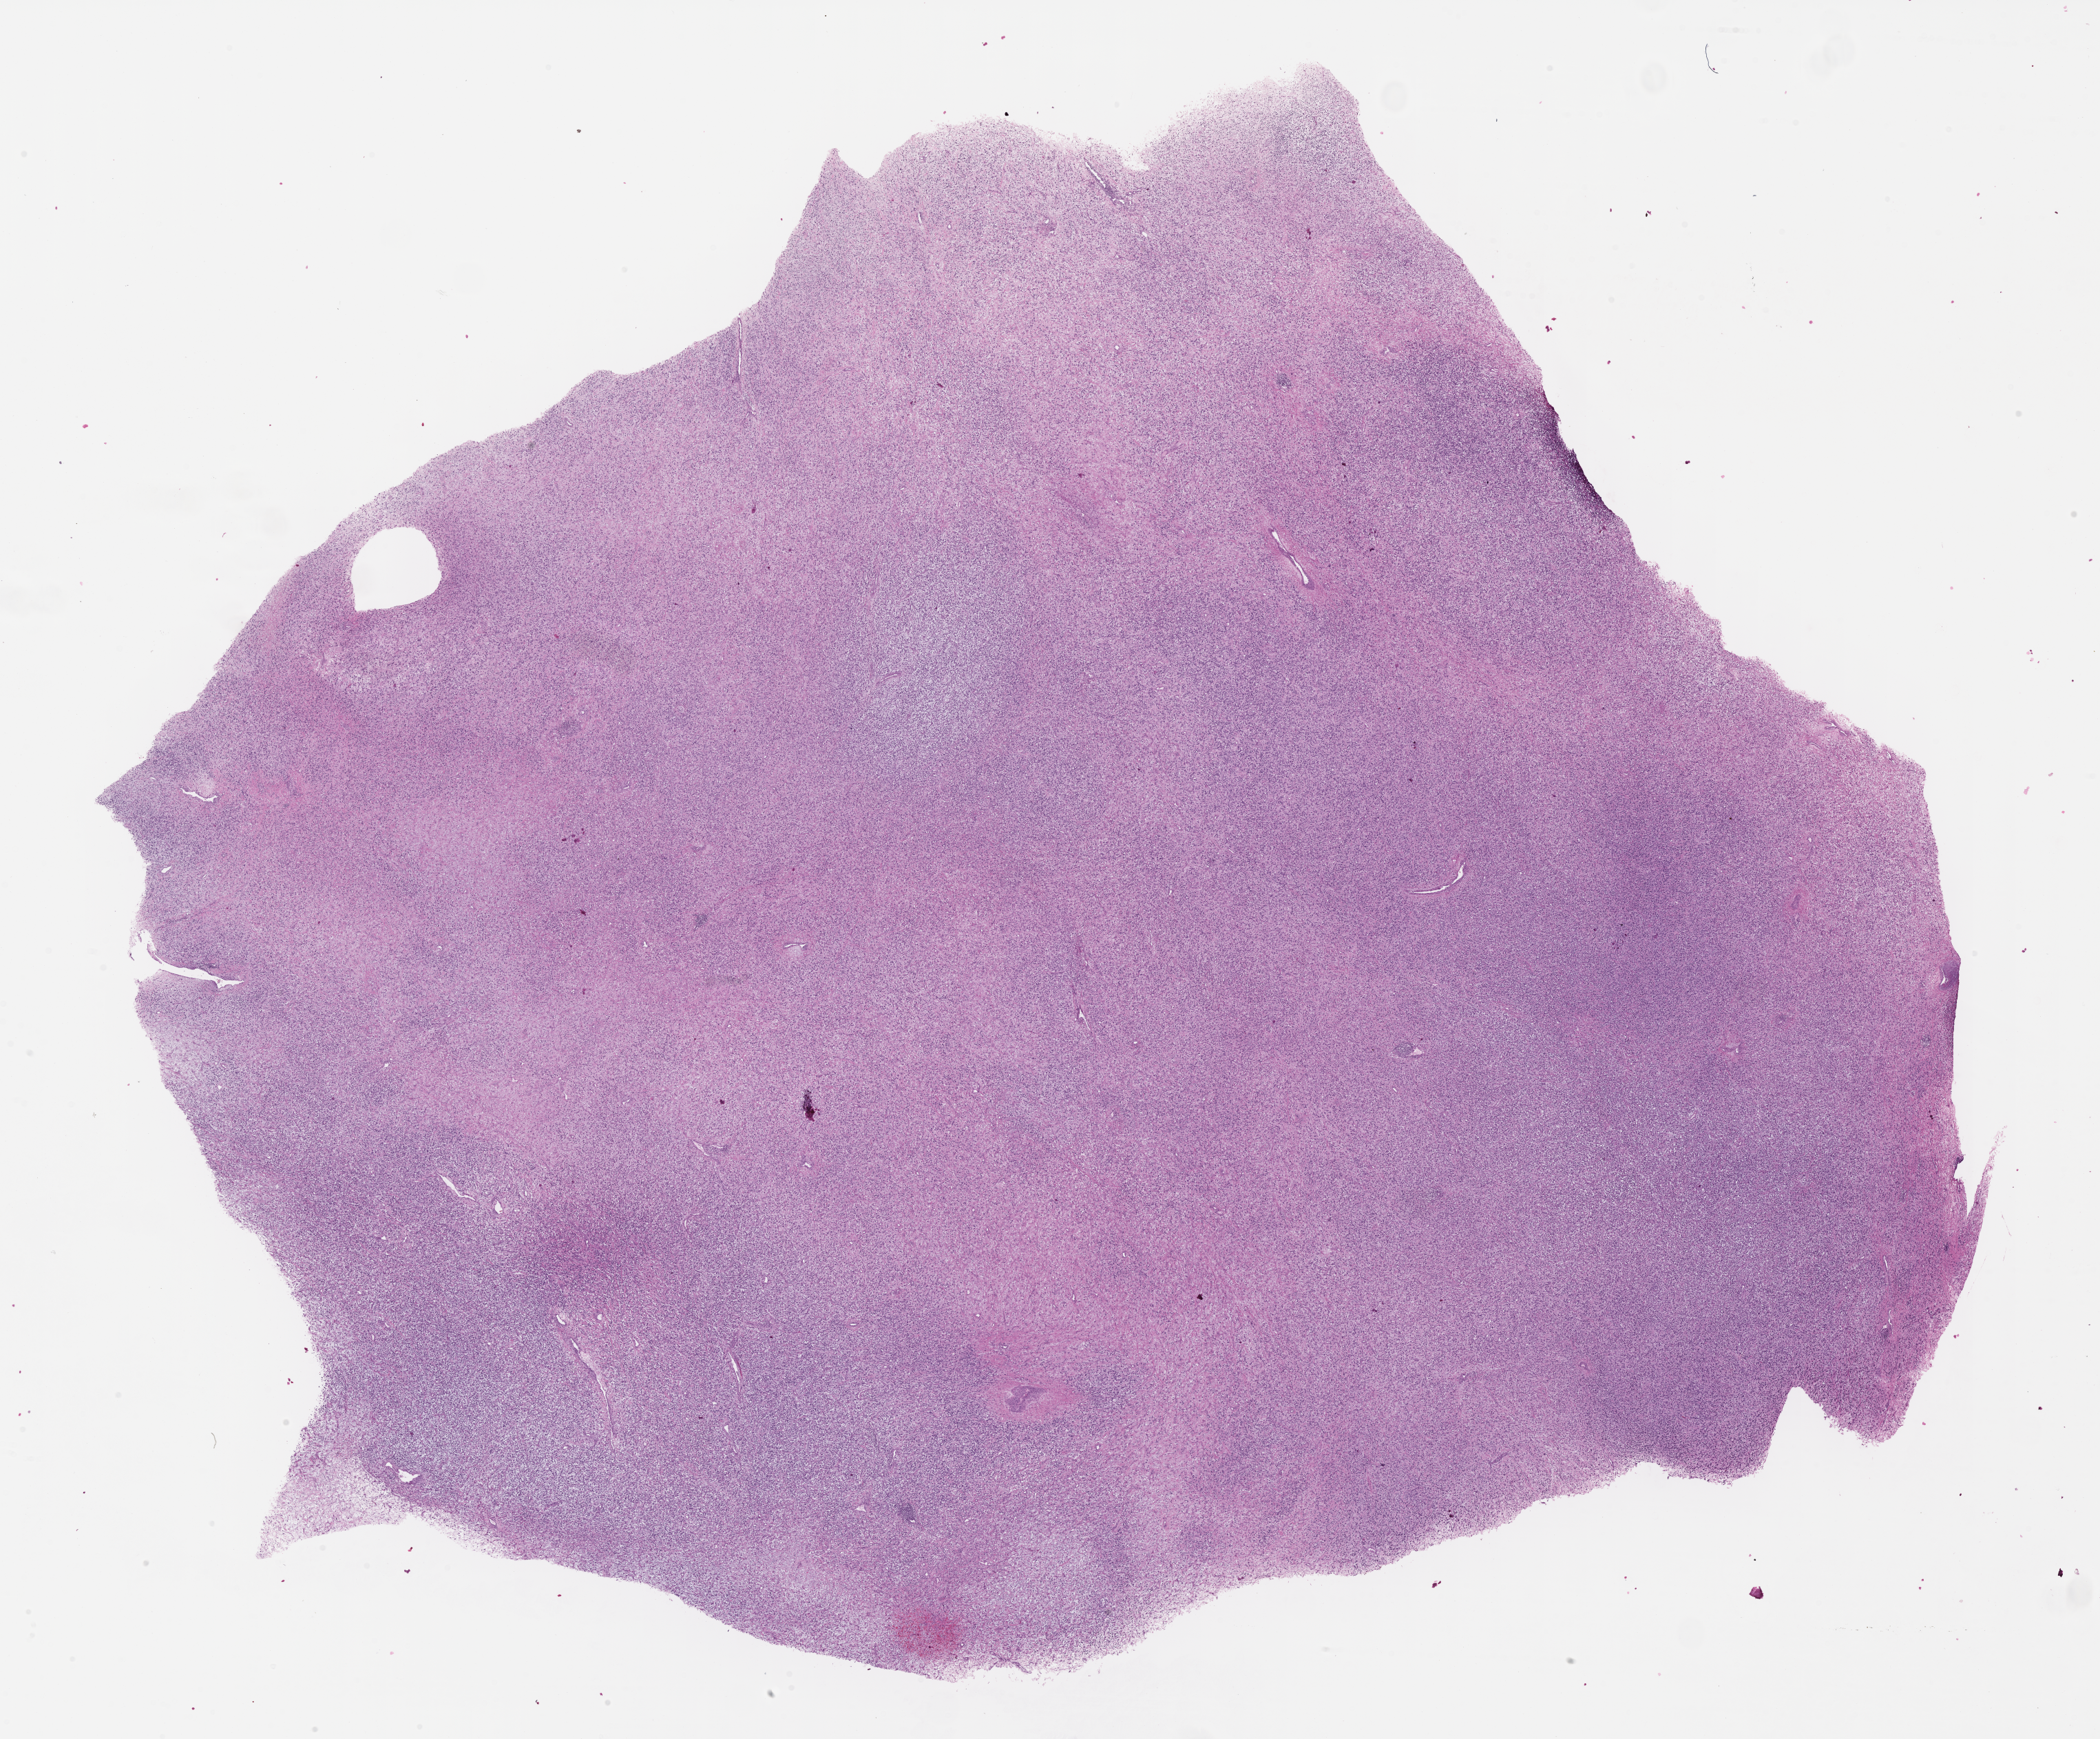
H&E whole-slide image of tumor tissue, shown as a low-resolution overview of the whole scanned area (about 24.7 x 20.4 mm). Formalin-fixed paraffin-embedded section. Sample anatomic site: testicle, left. Patient: male, age 13.7 years at diagnosis.
Metastatic status at presentation (as recorded): non-metastatic (confirmed). Stage (as recorded): 1. Primary site (case record): testis-paratesticular. Diagnosis: rhabdomyosarcoma; histological classification: embryonal rhabdomyosarcoma.